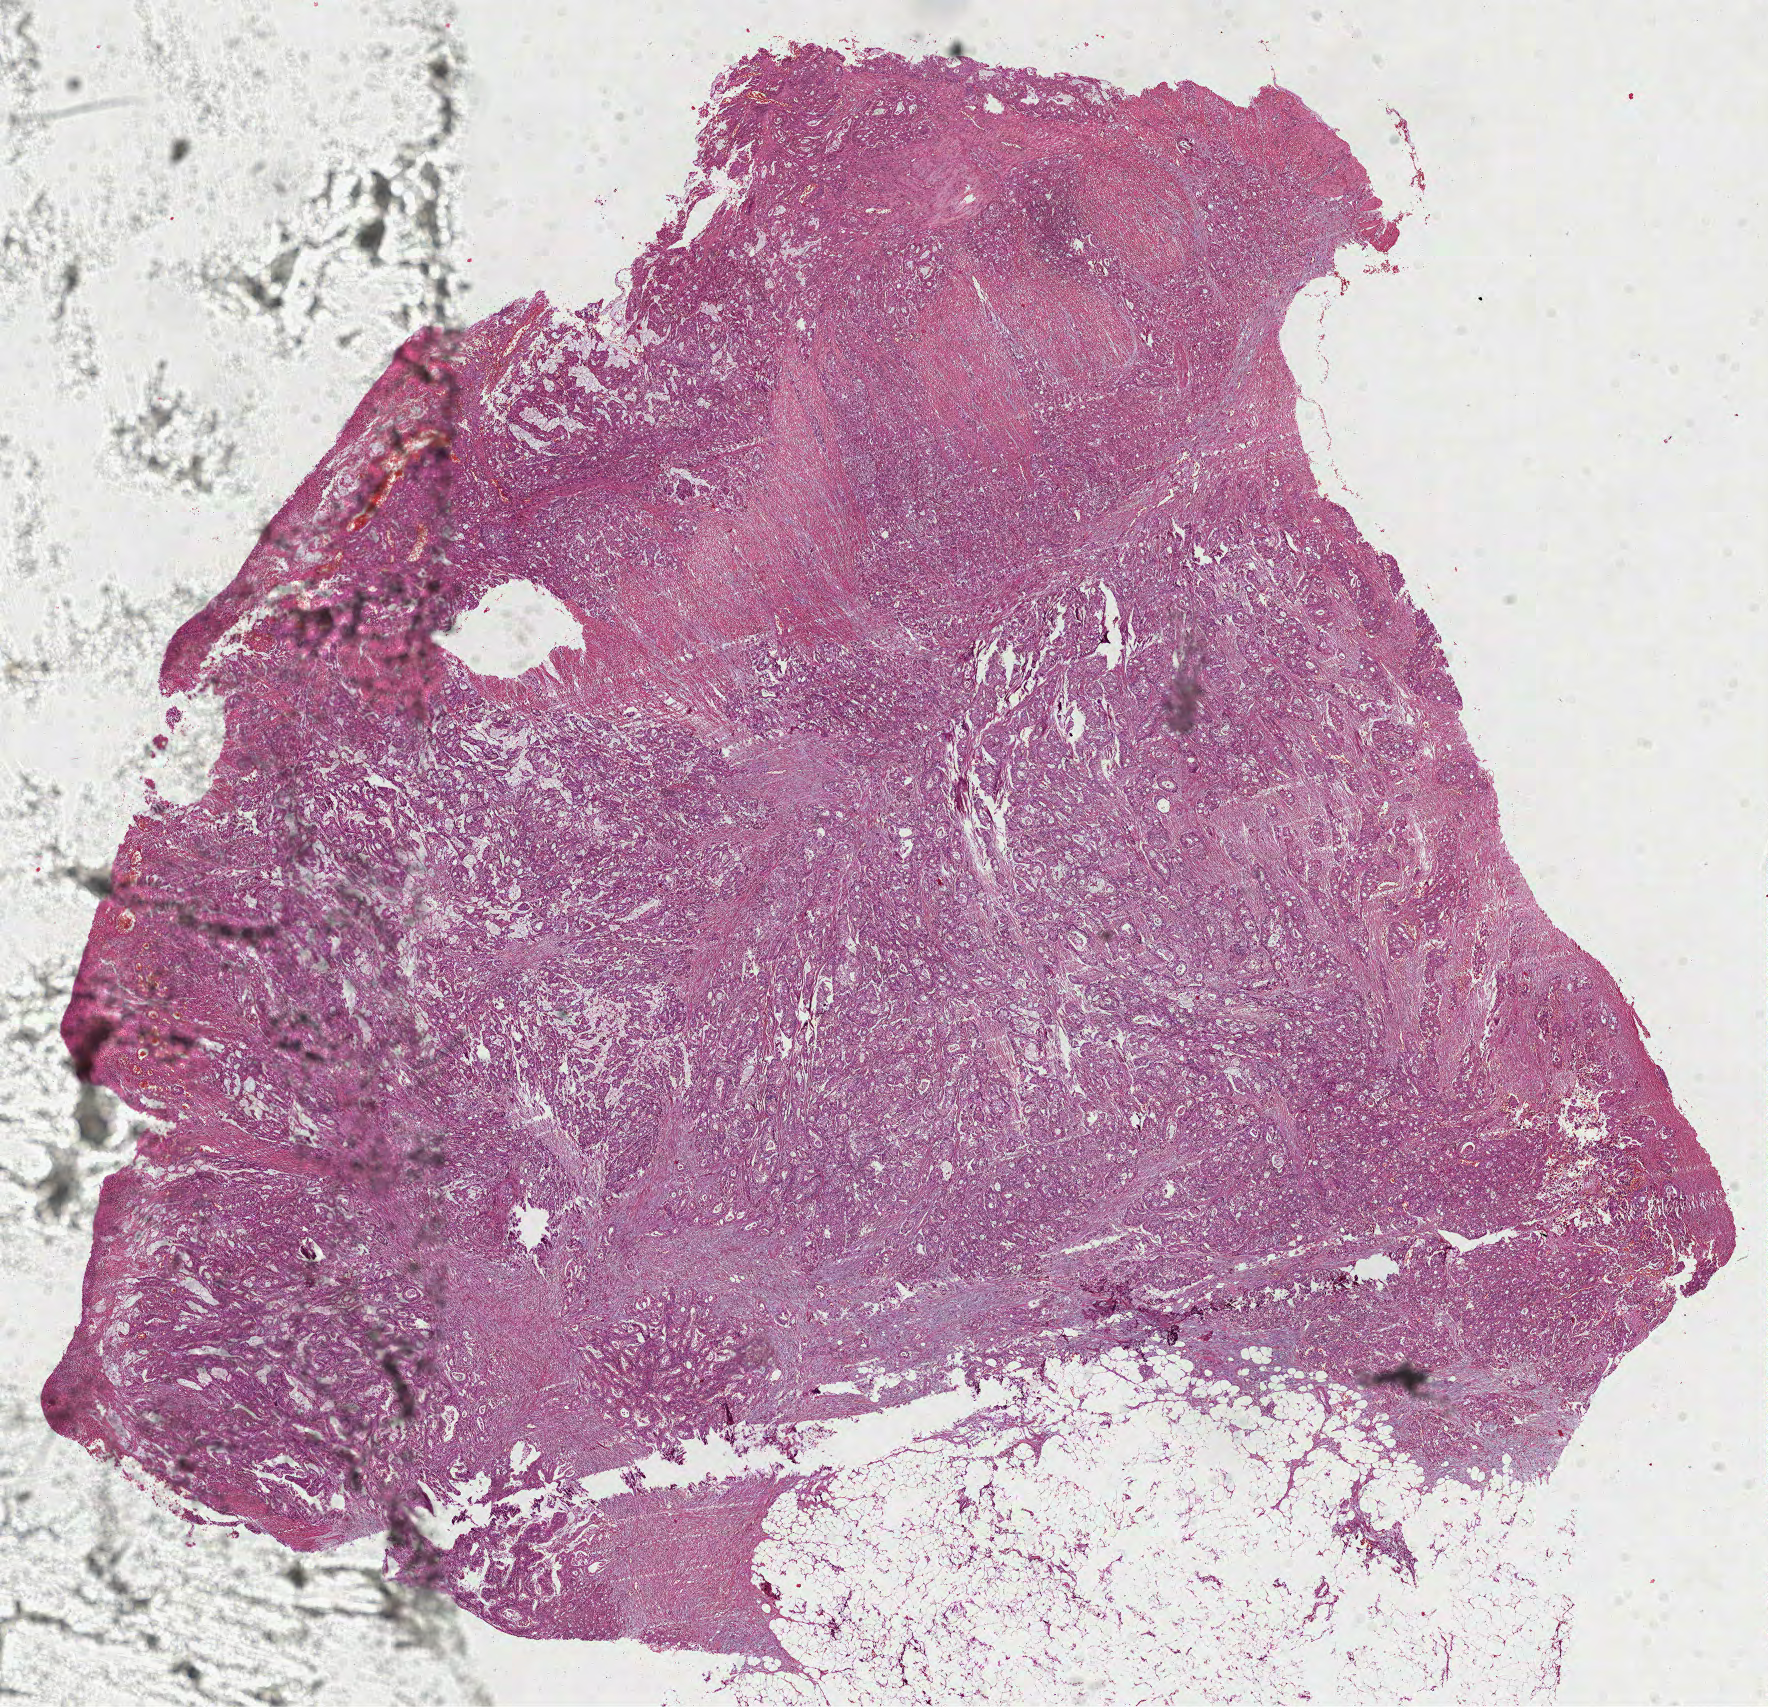
Hematoxylin and eosin (H&E) stained whole-slide image, a low-resolution overview of the entire scanned area, about 14.3 x 13.8 mm, formalin-fixed paraffin-embedded (FFPE) diagnostic section, primary tumour sample from the rectum. Male patient; age at initial diagnosis 51 years.
Pathologic diagnosis: Mucinous adenocarcinoma.